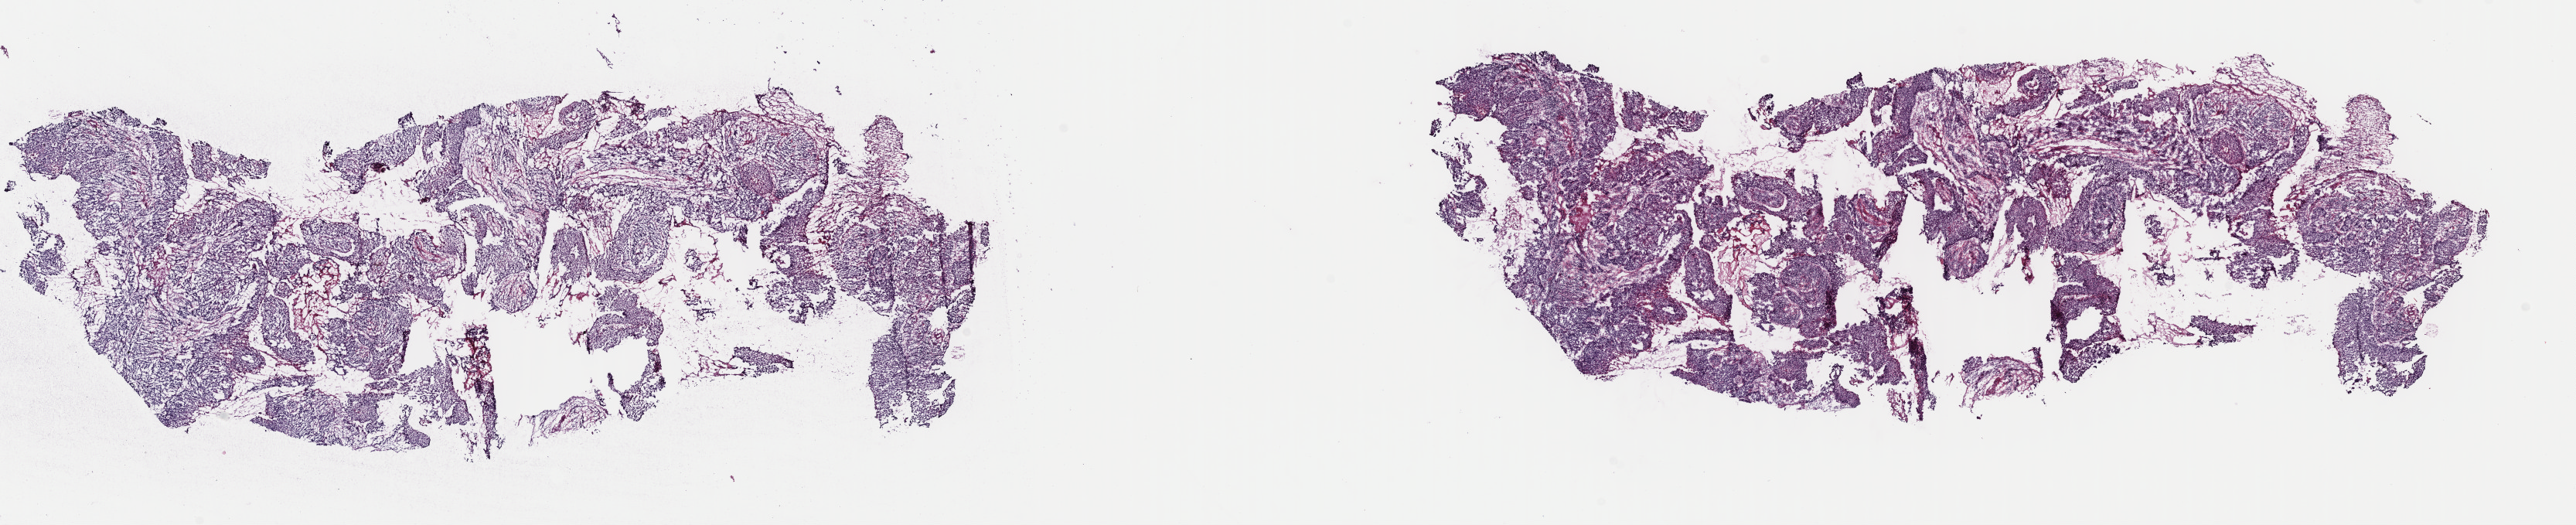
Digitized H&E-stained tissue section (whole slide), shown as a low-resolution overview of the whole scanned area (about 26.3 x 5.4 mm); frozen section from the top of the tissue portion; sample: primary tumour, cervix. Patient: female, age at initial diagnosis 46 years. Histologic grade: GX (grade cannot be assessed). Composition of this section per pathologist review: tumour cells 70%, tumour nuclei 70%, normal cells 0%, stromal cells 20%, necrosis 10%. Inflammatory infiltration, as recorded: lymphocyte infiltration 40%, monocyte infiltration 20%, neutrophil infiltration 20%.
Diagnosis: Squamous cell carcinoma, keratinizing, NOS (cervix uteri). FIGO stage: I.